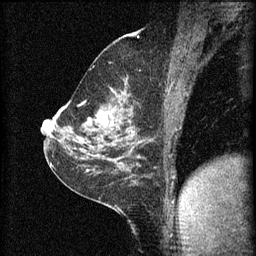
Breast MRI (dynamic contrast-enhanced), one sagittal slice; slice 37 of 60 in the series (ordered by position); 3 images stored at this slice position (order not interpretable as contrast timing); 1.5 T; TE 4.2 ms, TR 8.2 ms; 256 × 256 image matrix, field of view 180 × 180 mm. Female patient, age 59 years.
Structures marked on this image (semi-automatically segmented with operator editing):
- analysis volume of interest (the breast-tissue region the enhancement analysis was run in; not a lesion): box from (x=82, y=92) to (x=137, y=135) px
- tumour enhancement mask (voxels above the 70 % enhancement threshold inside the analysis volume of interest): (x=88, y=112)–(x=107, y=125)